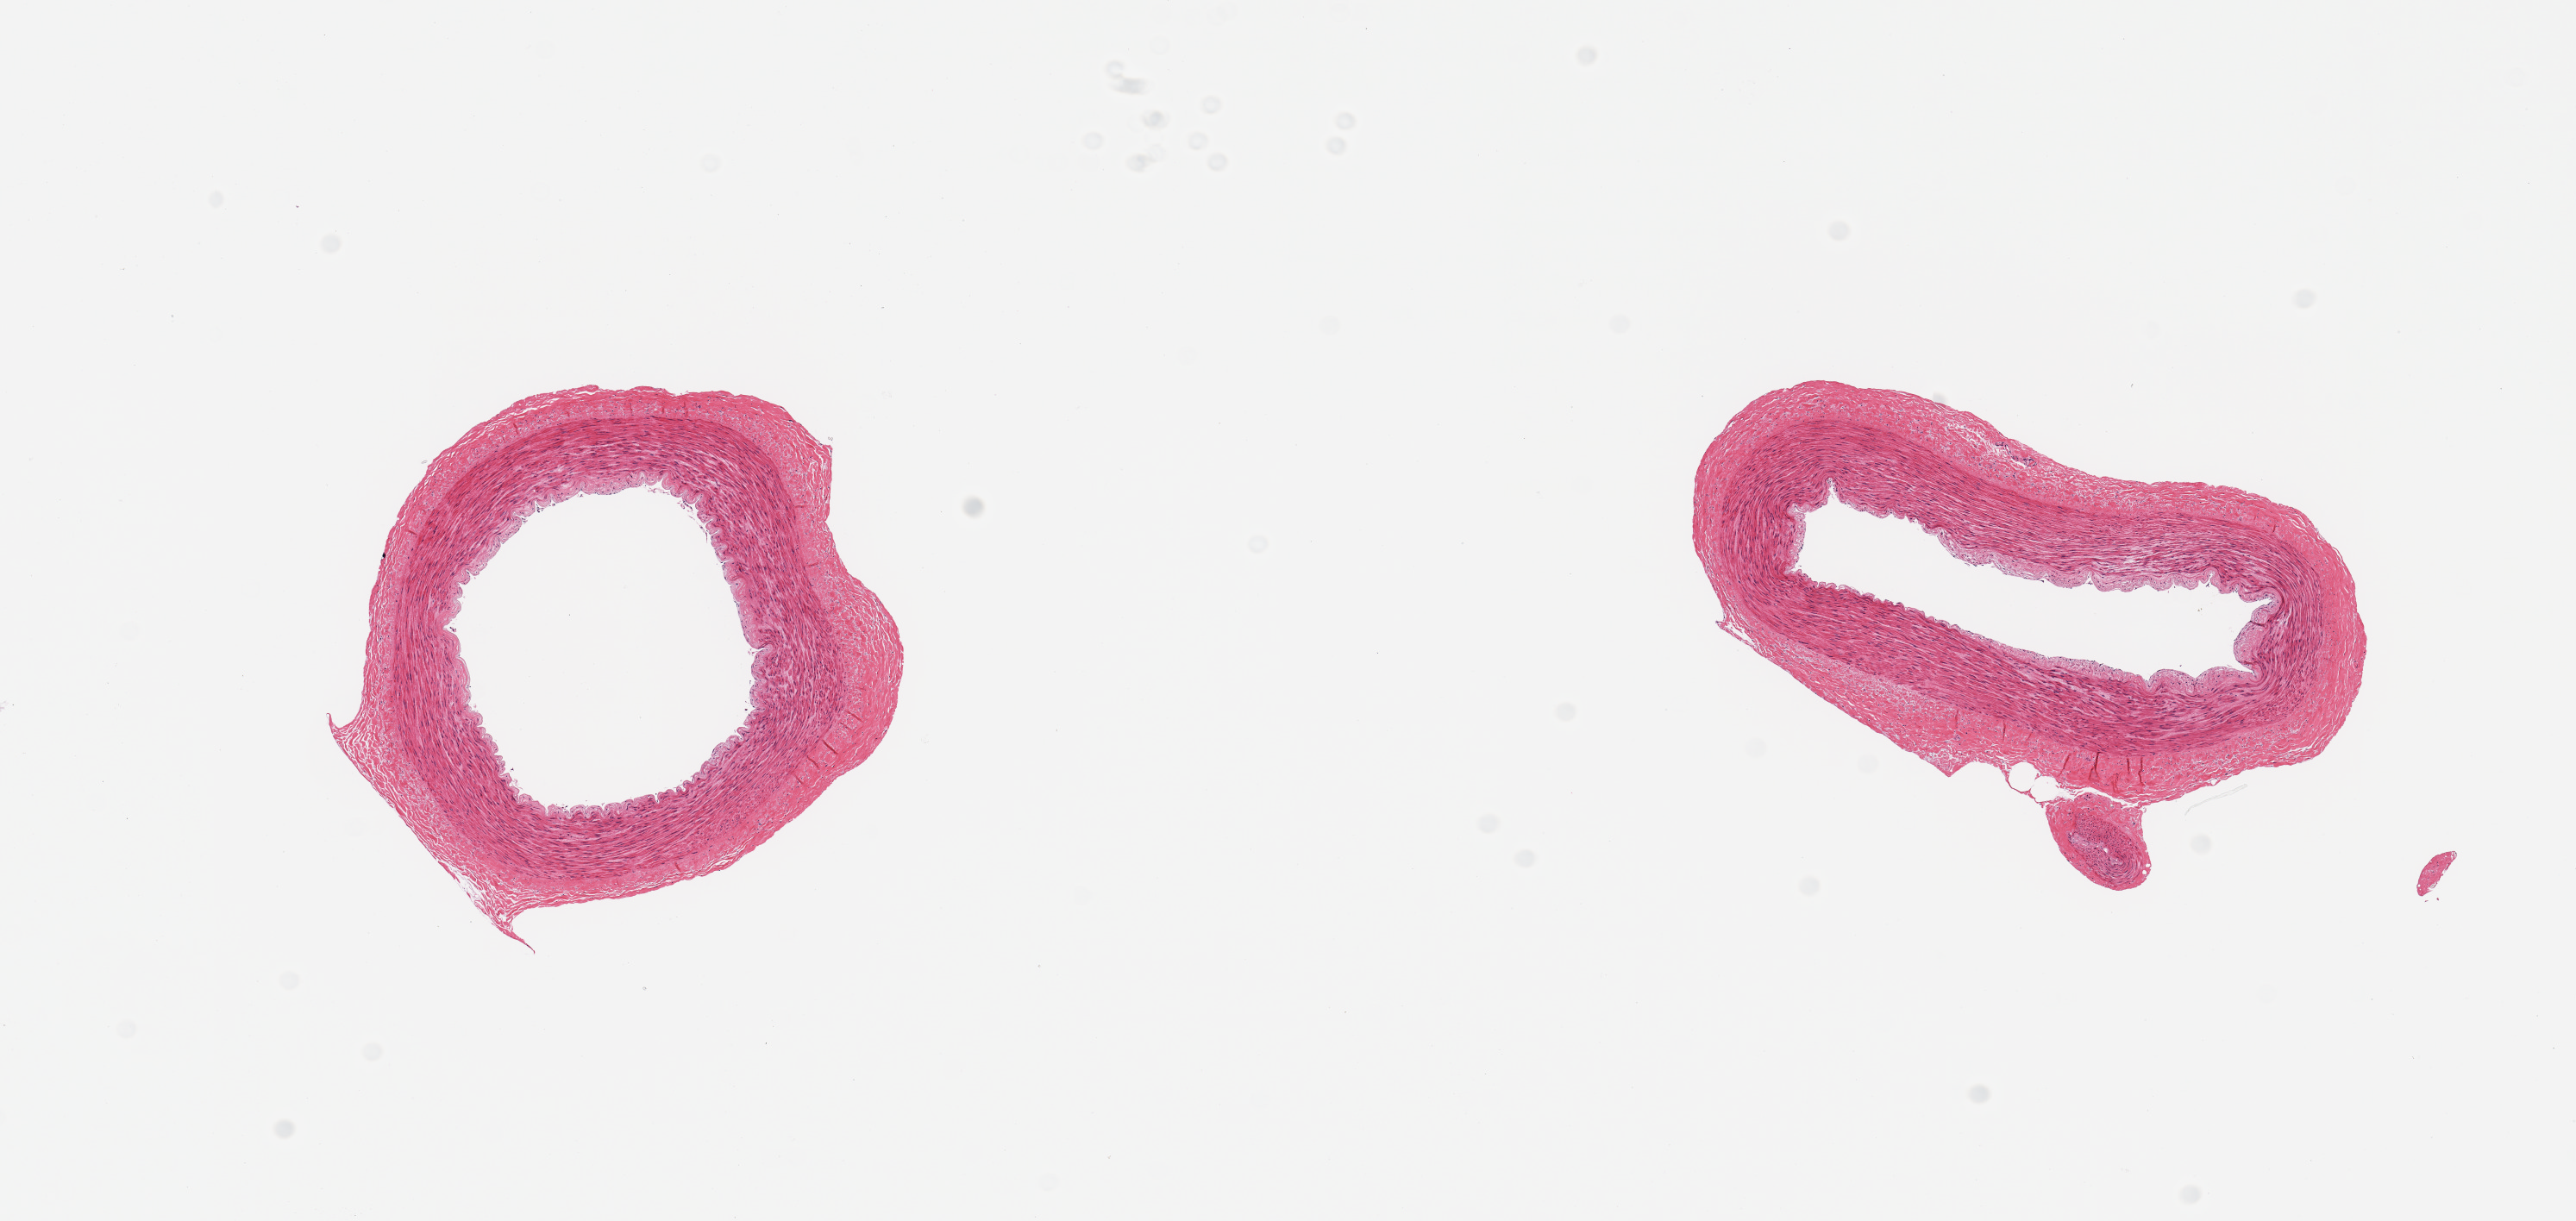
Whole-slide image, hematoxylin and eosin (H&E) stain — a low-resolution overview of the entire scanned area, about 11.8 x 5.6 mm (slide scanned at 20x); PAXgene-fixed paraffin-embedded (PFPE) section; section of tibial artery (target tissue); donor tissue sample.
Reviewer comment on this tissue sample: 2 pieces, no significant atherosis or adherent fat.